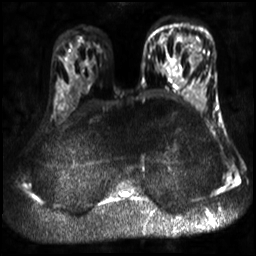
Breast MRI, one axial slice; slice 18 of 30 in the series (ordered by position); diffusion-weighted series; image 2 of 4 stored at this slice position (different b-values; order by instance number); 3 T; 256 × 256 image matrix, field of view 320 × 320 mm. Female patient.
Structures marked on this image (outlined manually by an expert reader):
- tumour on diffusion-weighted imaging: bounding box [x1, y1, x2, y2] px = [190, 42, 207, 66]